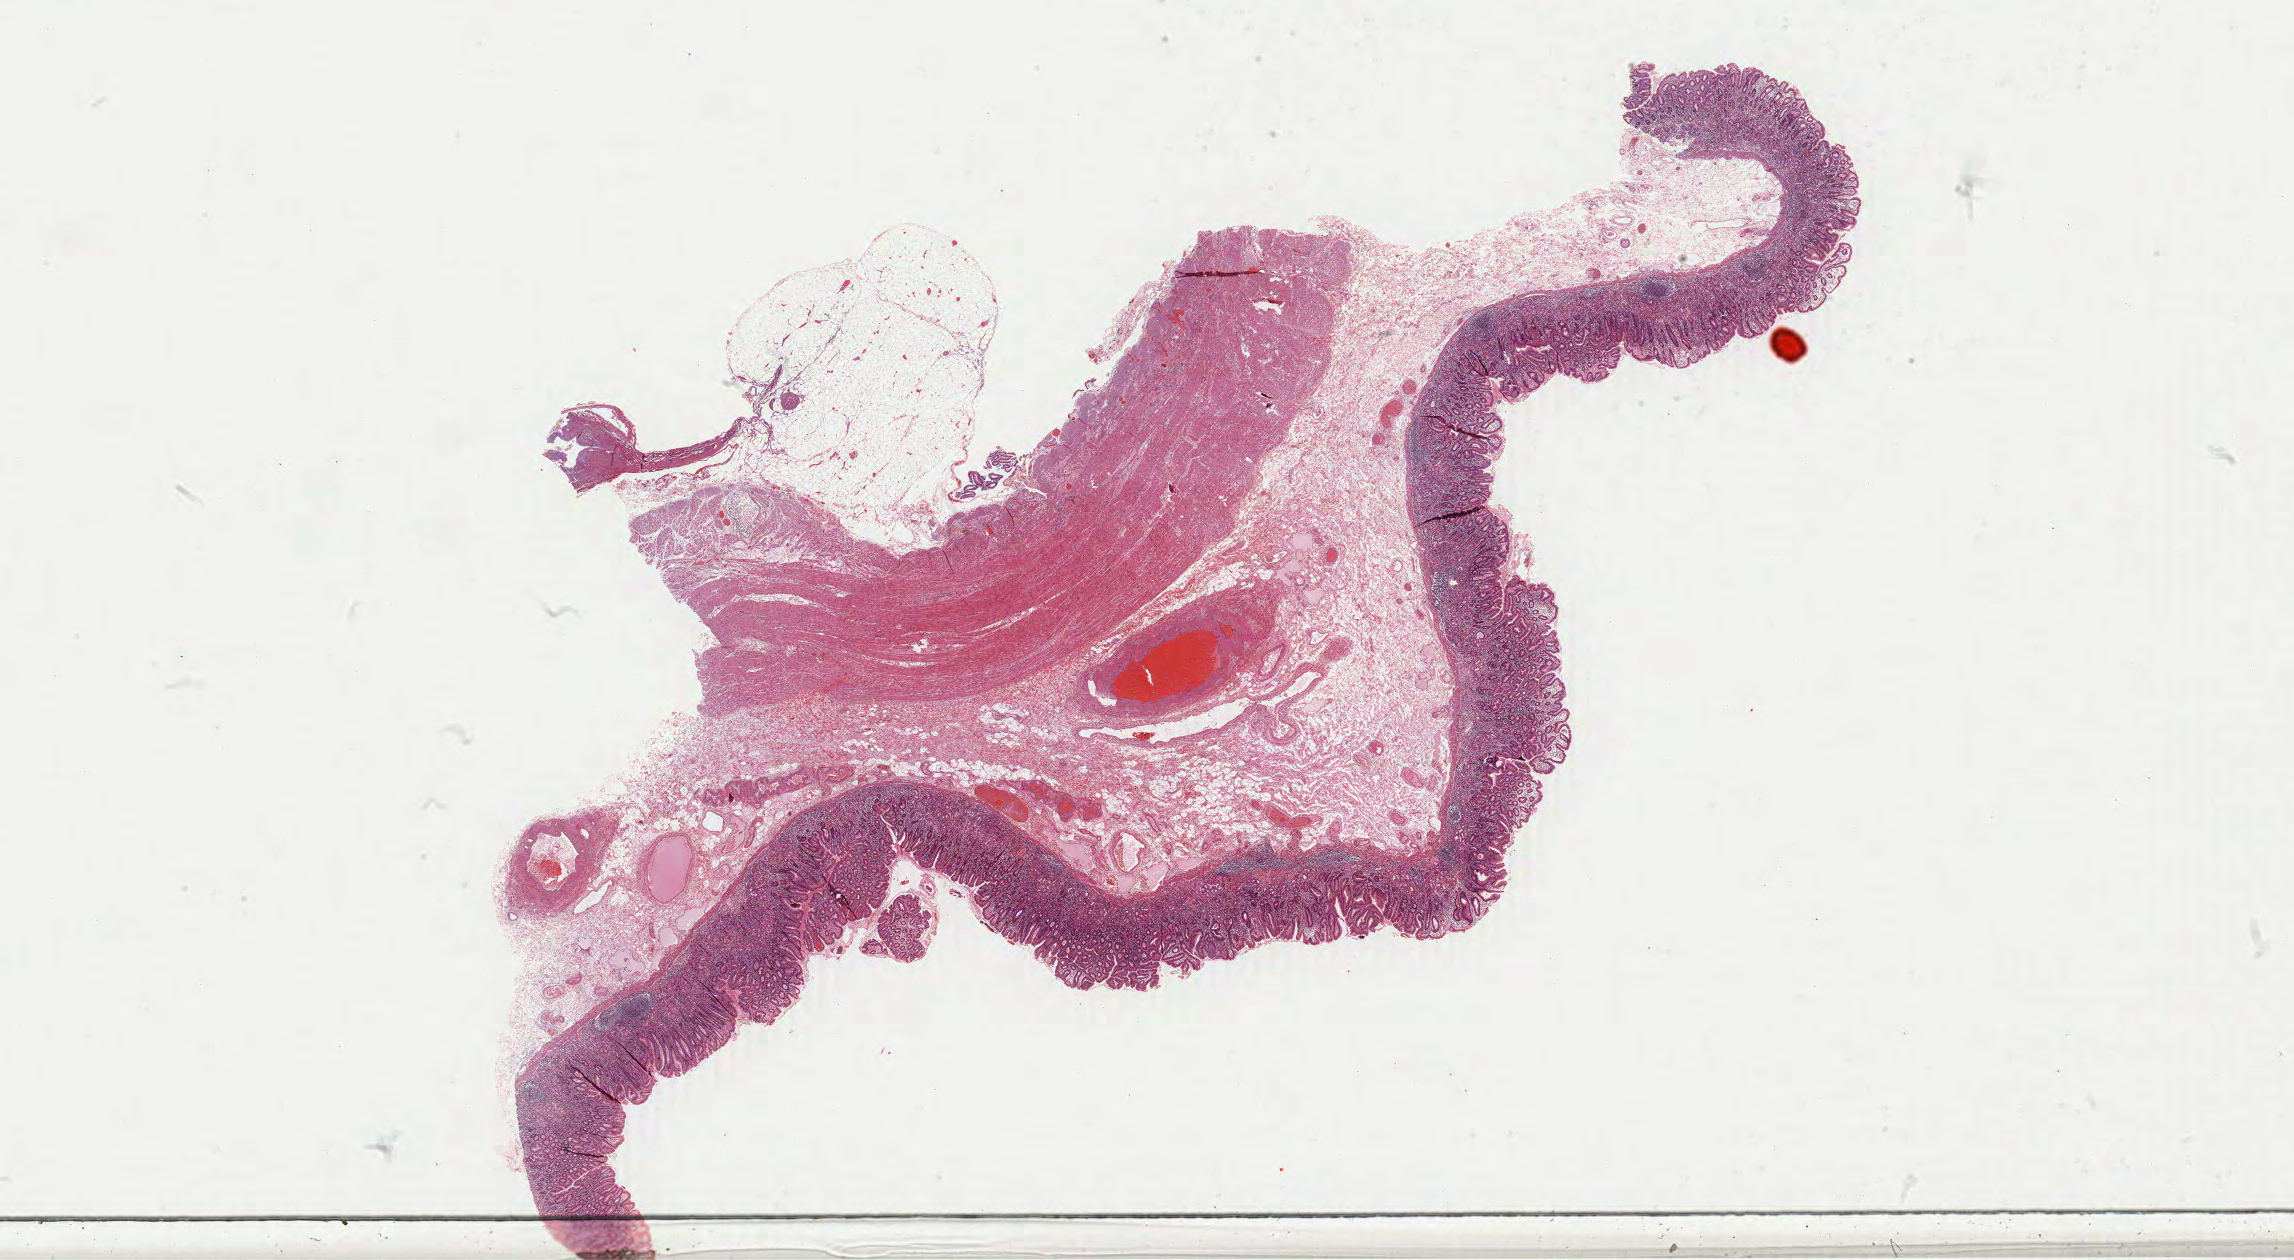
Whole-slide histology image, Hematoxylin and eosin (H&E) stained — a low-resolution overview of the entire scanned area, about 36.9 x 20.3 mm (acquisition: 40x scan); FFPE section; primary tumour sample from the stomach. Male patient; age at initial diagnosis 78 years. Histologic grade: G2 (moderately differentiated).
Lymph nodes positive (case pathology): 4 of 21 examined. AJCC pathologic stage: IIIA (6th edition). Pathologic diagnosis: Mucinous adenocarcinoma (fundus of stomach).